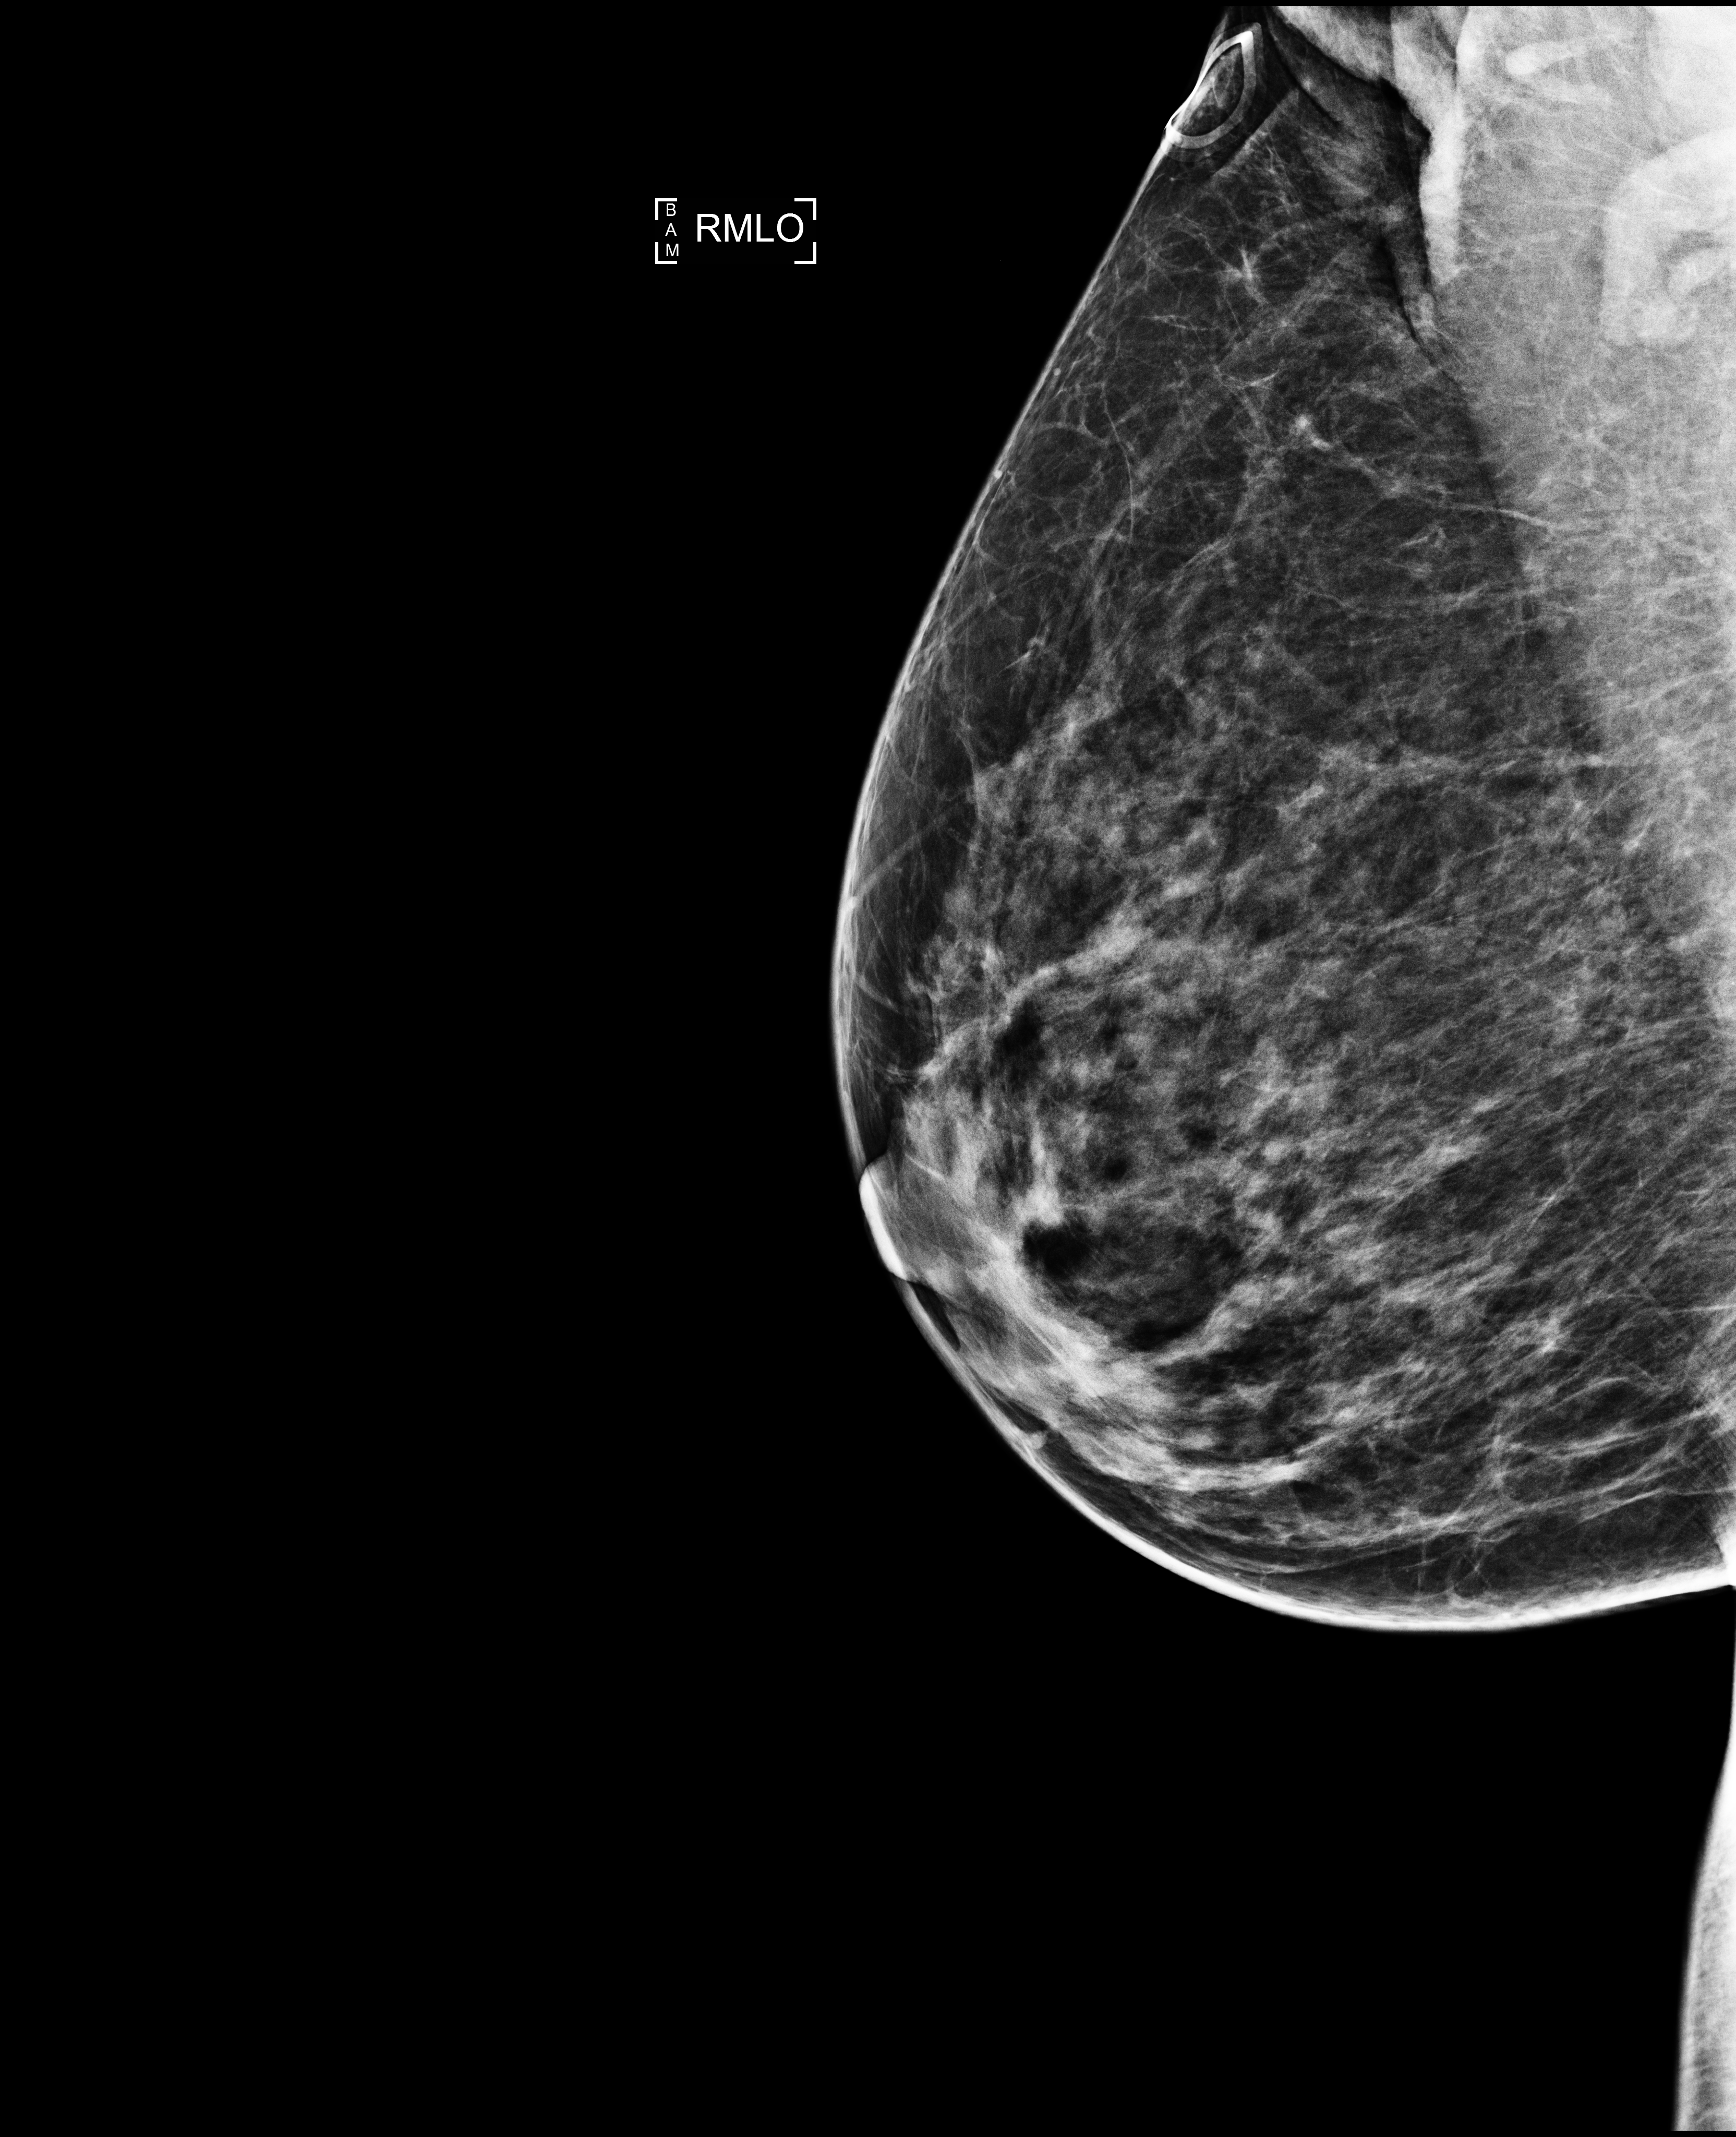
Annual screening mammography examination; system: Selenia Dimensions. Female patient, age 44 years.
Image type: full-field digital mammogram. Breast: right. Projection: MLO view.